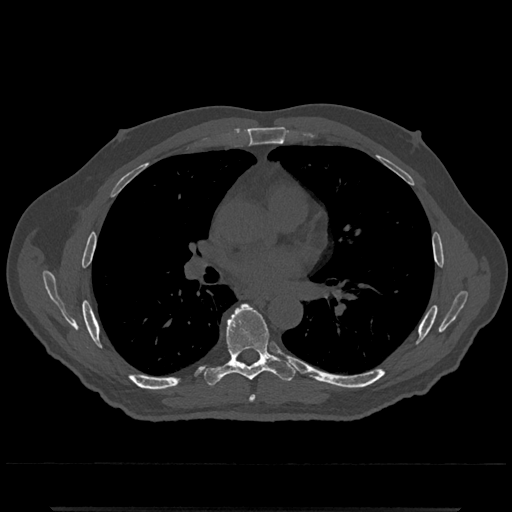
CT including the spine, one axial slice. Slice 726 of 797 in the series (ordered by position). Reconstruction kernel Br40s/3. 120 kVp. Bone window (W 1800 / L 400 HU). 0.5 mm slice thickness. 512 × 512 image matrix, field of view 393 × 393 mm. Patient: male, 67 years. From the clinical record (not read from this slice): primary cancer: prostate.
Annotated regions visible in this slice (semi-automatic segmentation, software-assisted and operator-edited):
- T6 vertebra: bounding box (x1, y1, x2, y2) in pixels: (249, 395, 256, 402)
- T7 vertebra: (205, 304, 295, 386)